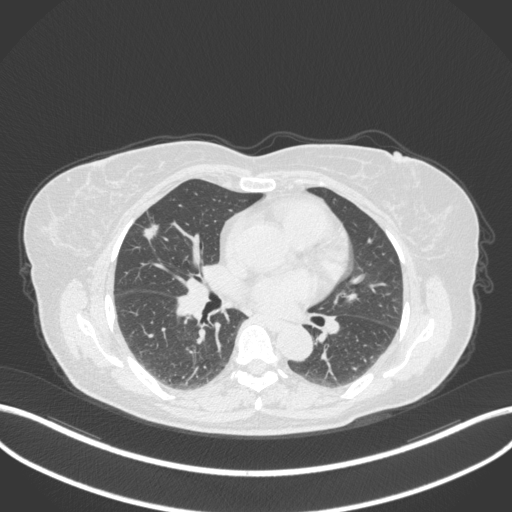
Chest CT, one axial slice; position 173 of 310 along the scan axis; 120 kVp; lung window (W 1500 / L -600 HU); 1 mm slice thickness; 512 × 512 image matrix, field of view 400 × 400 mm. Female patient, age 55 years. Case-level facts recorded for this patient, not image findings: clinical TNM (as recorded): T1b N0 M0; histopathological grade: G2.
Annotated regions visible in this slice (rectangle marked by the reading radiologist):
- lung tumour (recorded histology: adenocarcinoma): bounding box (x1, y1, x2, y2) in pixels: (136, 220, 162, 242)